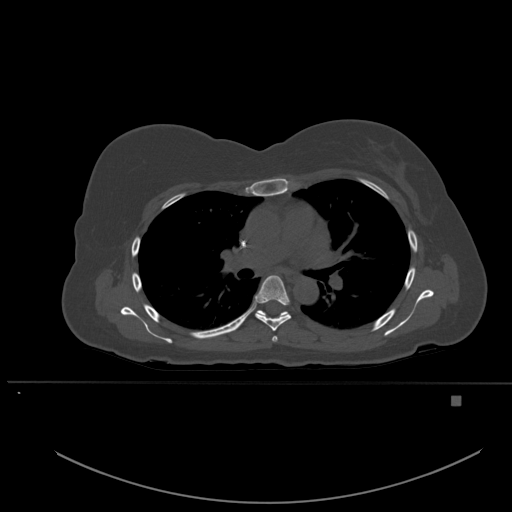
CT including the spine, one axial slice; position 362 of 651 along the scan axis; bone window (W 1800 / L 400 HU); 1.5 mm slice thickness; 512 × 512 image matrix, field of view 443 × 443 mm. Patient: female, 49 years. Case-level facts recorded for this patient, not image findings: primary cancer: breast; vertebrae with lytic lesions (as recorded): L3, T12, L4.
Annotated regions visible in this slice (semi-automatically segmented with operator editing):
- T4 vertebra: bounding box <272,336,278,342> (left, top, right, bottom; pixels)
- T5 vertebra: <255,275,291,331>
- T6 vertebra: <256,310,288,317>